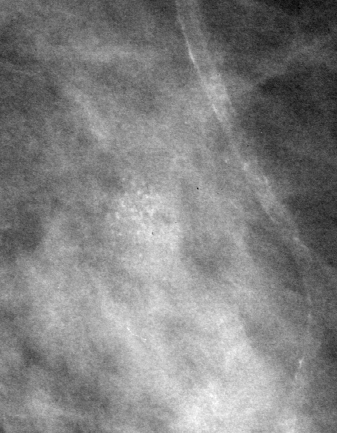
Region of interest cut from a scanned film mammogram (one marked finding), left breast, MLO view, BI-RADS breast density category 2 (scale 1–4).
Finding: calcifications, morphology amorphous, distribution clustered; BI-RADS assessment category 4; pathology result (as recorded, not read from the image): benign.